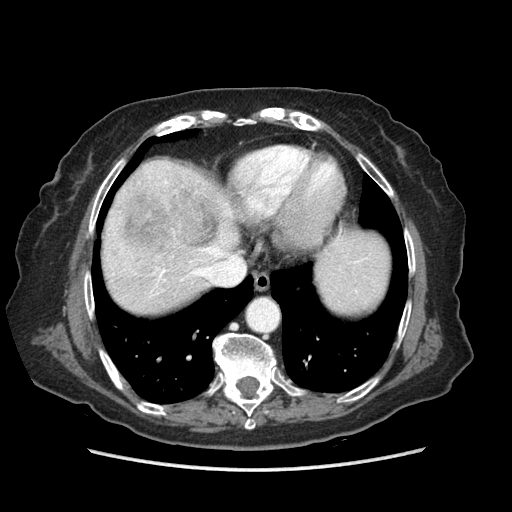
Contrast-enhanced abdominal CT (liver protocol), one axial slice; position 73 of 89 along the scan axis; soft-tissue window (W 400 / L 40 HU); 512 × 512 image matrix, field of view 360 × 360 mm. From the clinical record (not read from this slice): diagnosis: hepatocellular carcinoma (patient treated with transarterial chemoembolisation; whether this scan precedes or follows treatment is not stated here); TNM stage (as recorded): Stage-IIIA; Child-Pugh class: A; tumour differentiation: well differentiated; tumour nodularity: multinodular.
Structures marked on this image (semi-automatic segmentation, software-assisted and operator-edited):
- abdominal aorta: bounding box <248,300,277,330> (left, top, right, bottom; pixels)
- liver parenchyma outside the tumour (the mass and vessels are separate outlines, so this box may not span the whole liver): <102,158,388,312>
- mass: <118,182,219,267>
- liver vessels: <157,180,357,281>